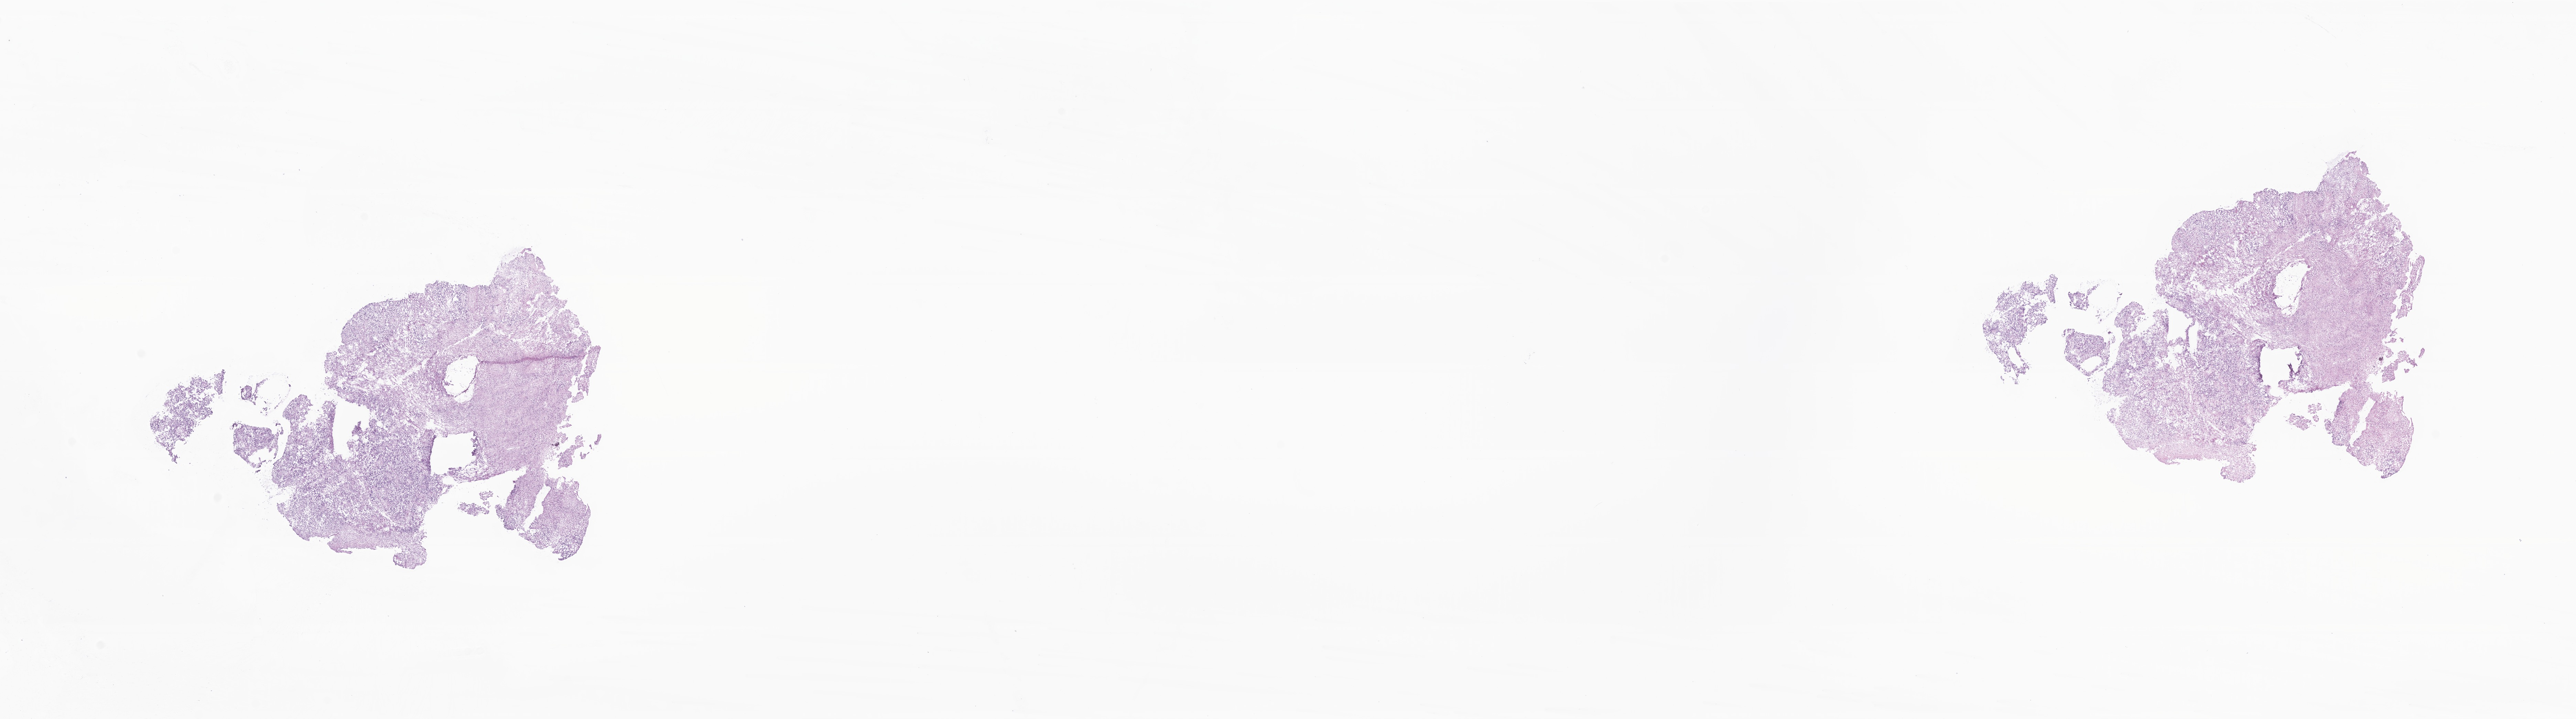
Whole-slide image, haematoxylin and eosin stain of tumor tissue from the brain — a low-resolution overview of the entire scanned area, about 31.6 x 8.8 mm. Cryosection (OCT / tissue freezing medium). Male patient, age 525 days (about 1.4 years).
Recorded diagnosis: Ependymoma, NOS.